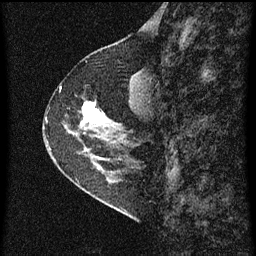
Breast MRI (dynamic contrast-enhanced), one sagittal slice. Slice 24 of 60 in the series (ordered by position). Dynamic contrast-enhanced series, image 2 of 3 at this slice position (ordered by acquisition). 1.5 T. TE 4.2 ms, TR 8 ms. 256 × 256 image matrix, field of view 180 × 180 mm. Female patient, age 56 years.
Outlined on this slice (semi-automatically segmented with operator editing):
- analysis volume of interest (the breast-tissue region the enhancement analysis was run in; not a lesion): bounding box [x1, y1, x2, y2] px = [49, 96, 110, 159]
- tumour enhancement mask (voxels above the 70 % enhancement threshold inside the analysis volume of interest): [83, 104, 106, 123]